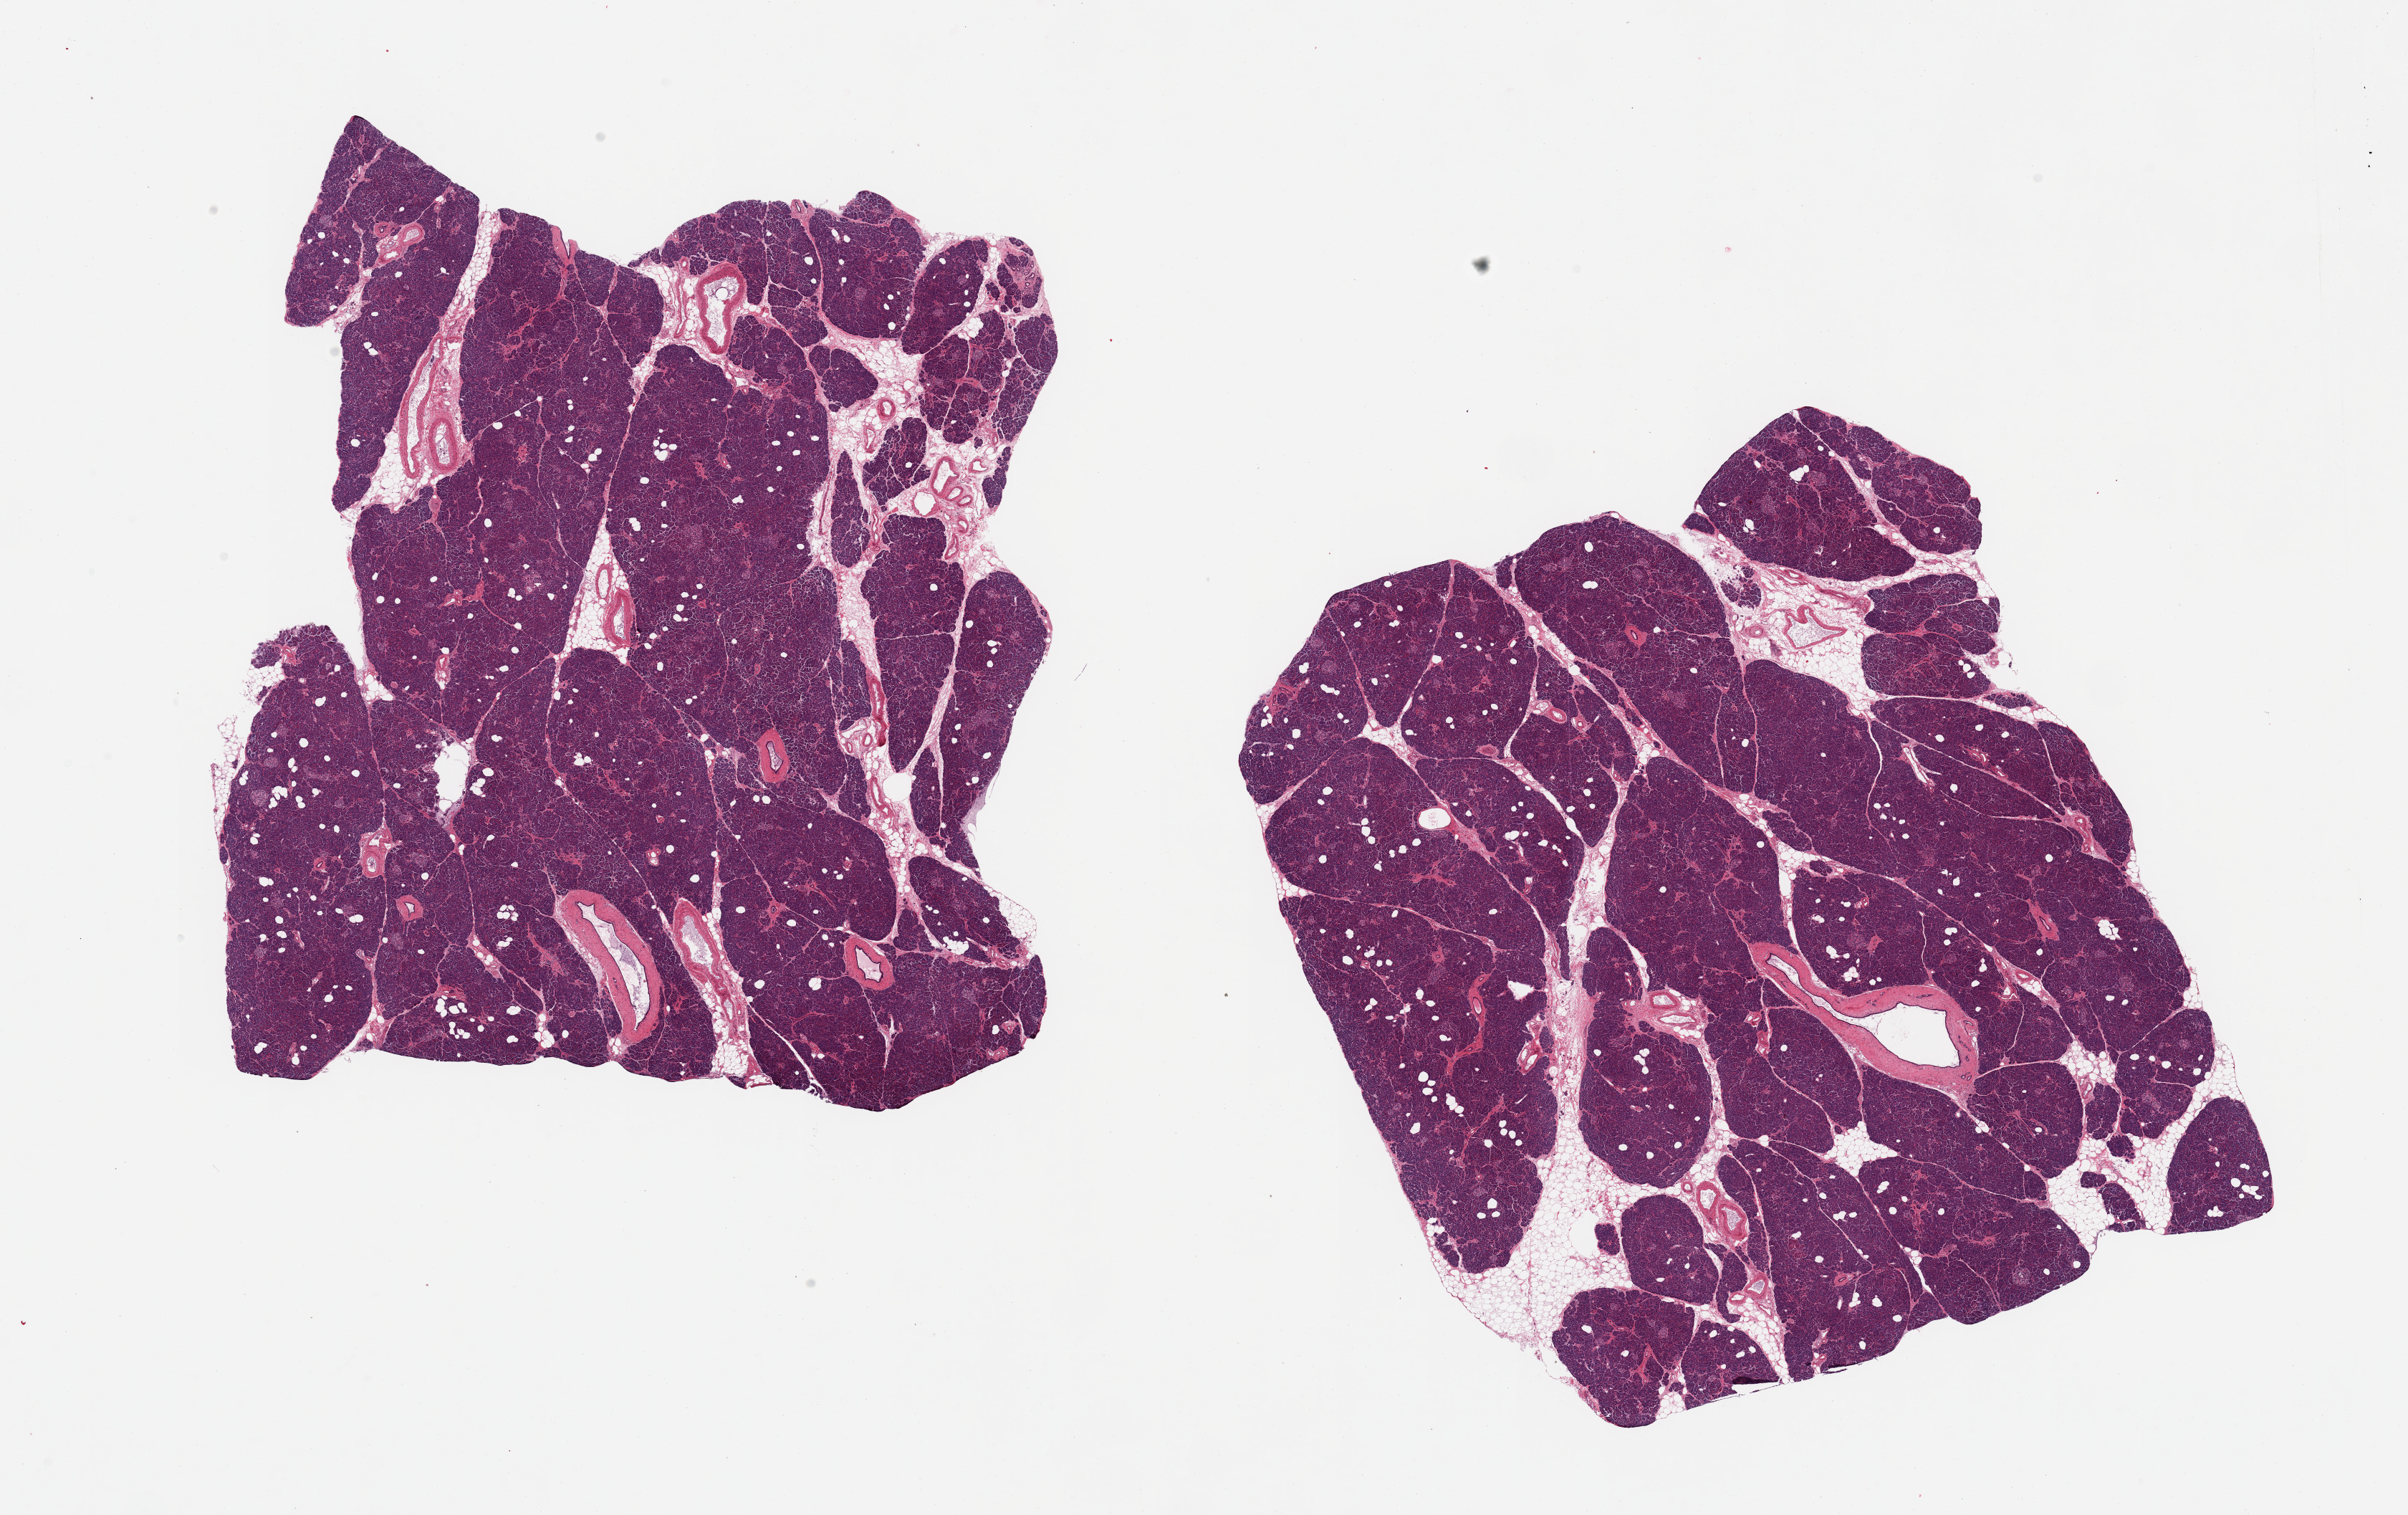
Digitized H&E-stained section, whole scanned area (about 26.6 x 16.7 mm) shown as a low-resolution overview; PAXgene-fixed paraffin-embedded (PFPE) section; target tissue: pancreas; tissue donor sample. Donor sex: female.
Pathologist's review note for this sample: 2 pieces, islets well preserved.